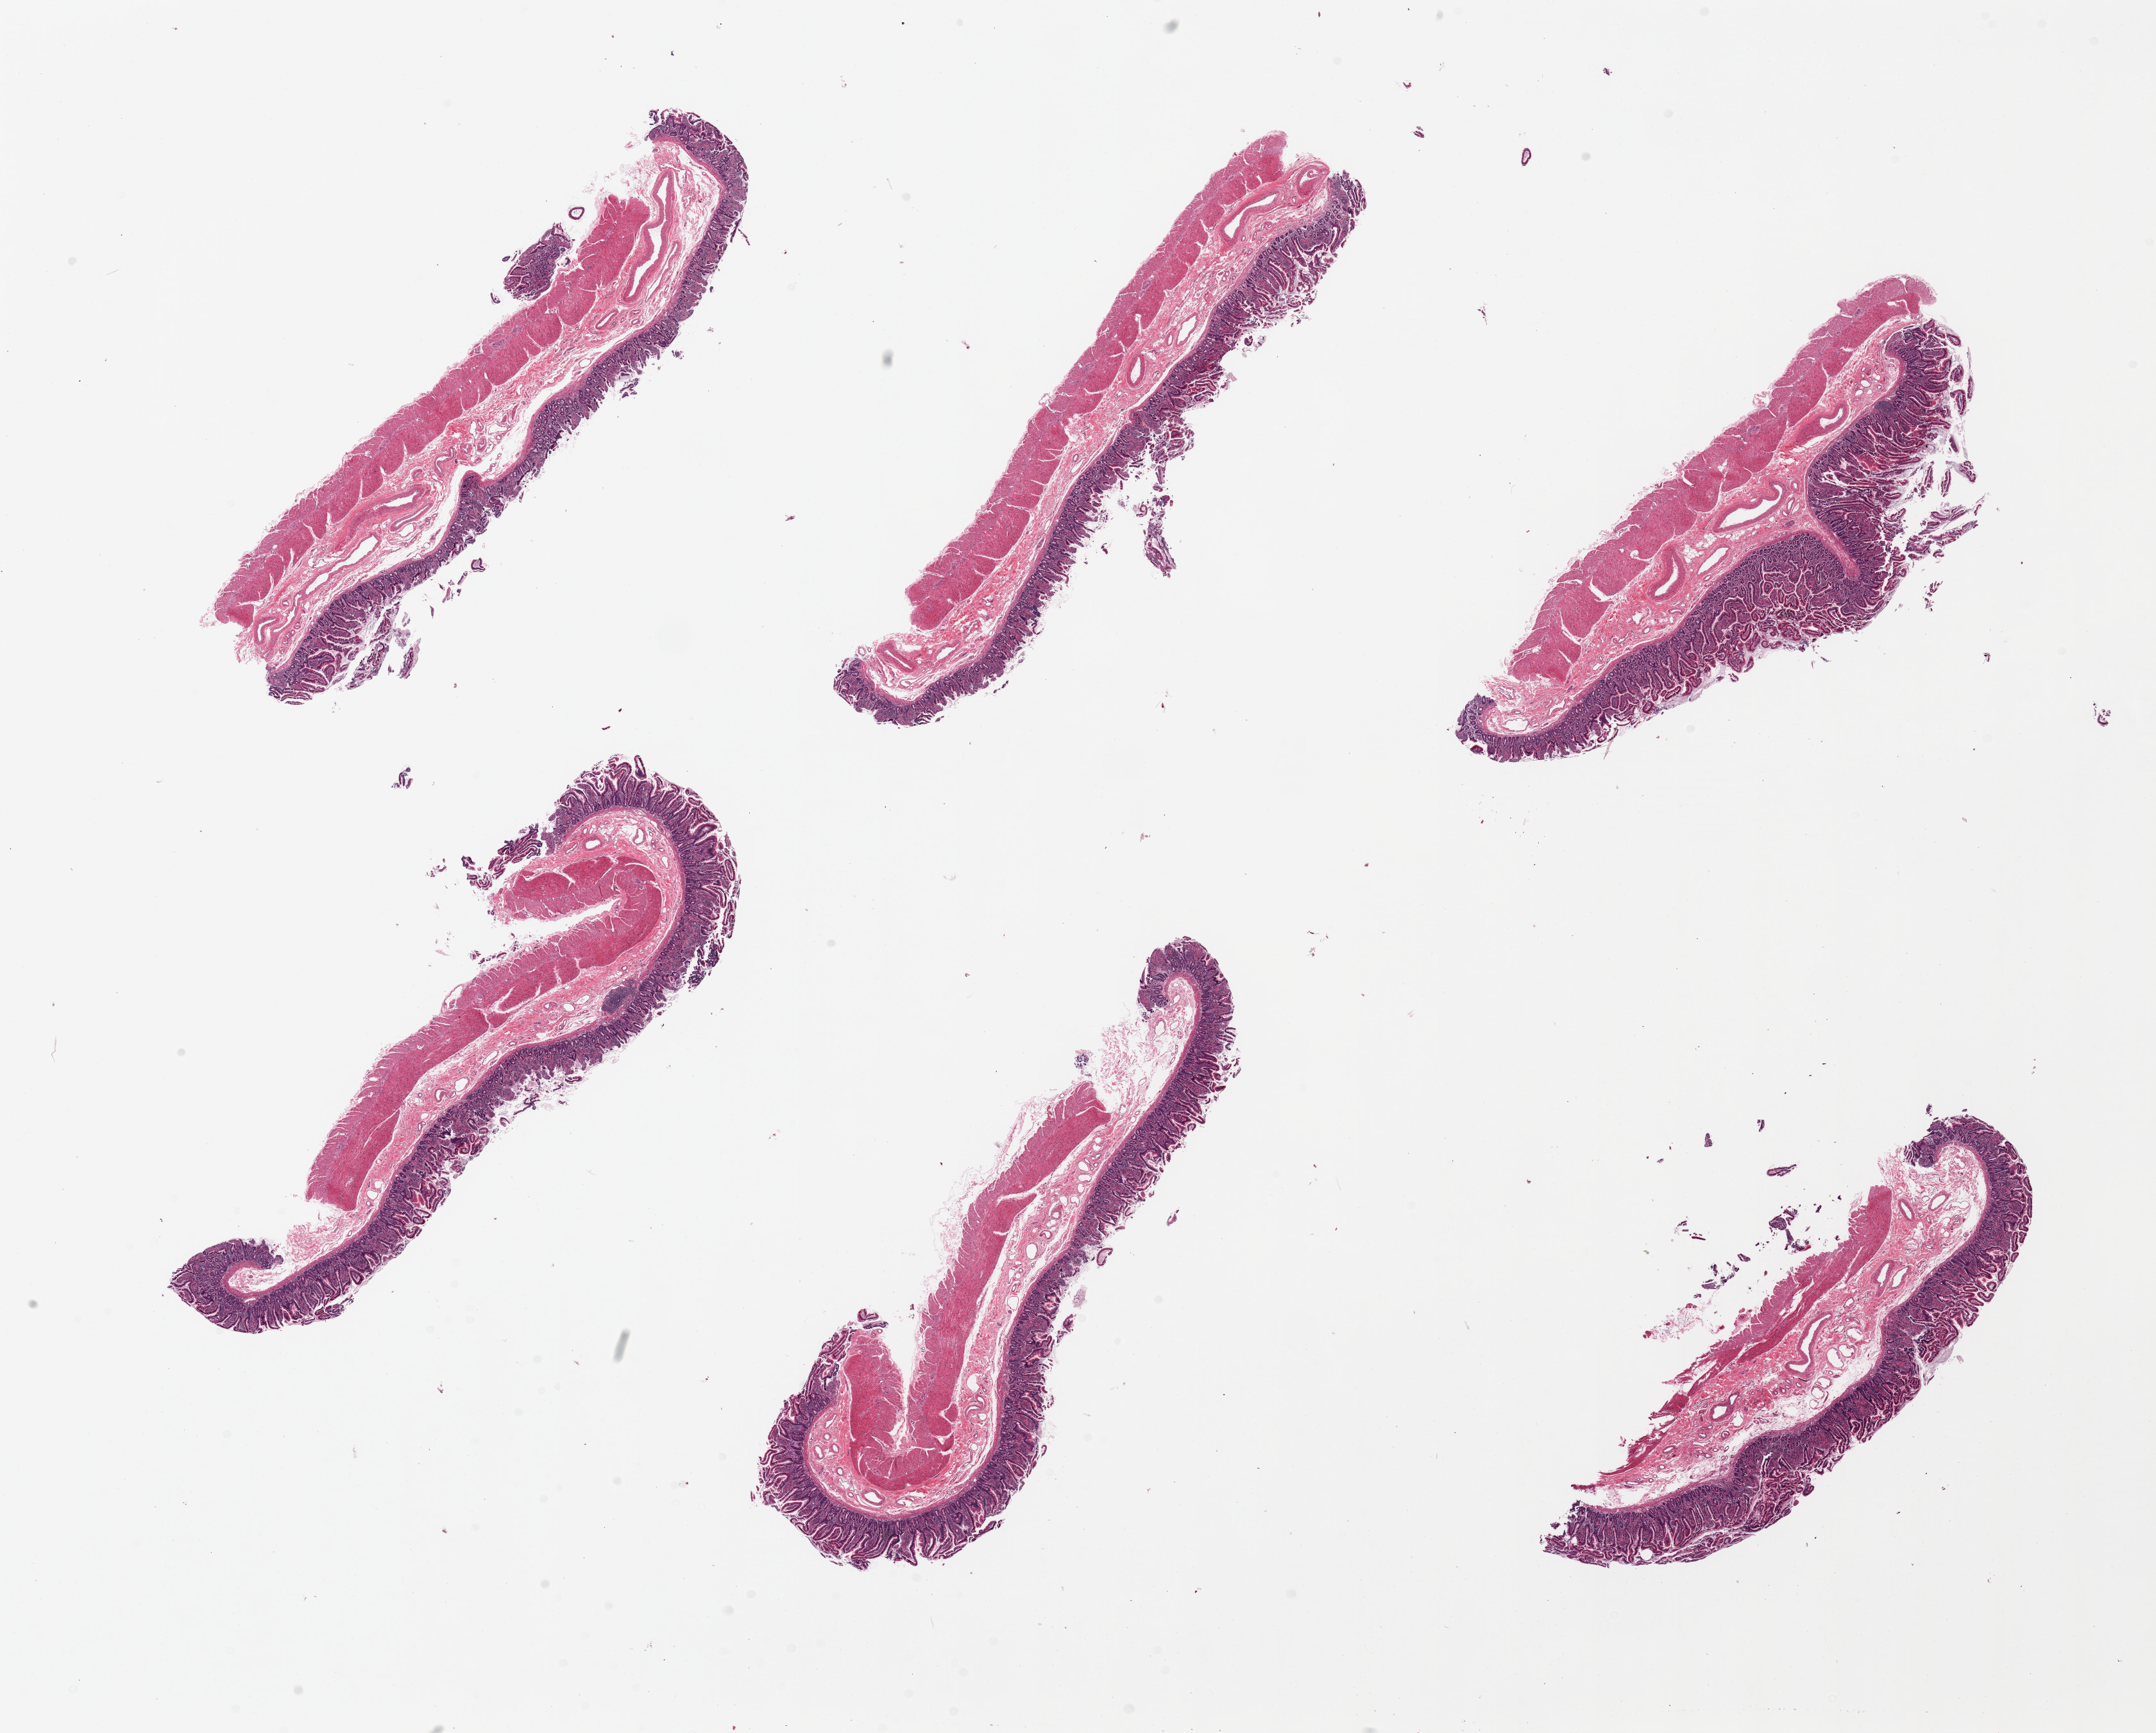
Digitized H&E-stained section — low-resolution overview of the scanned area, about 26.6 x 21.4 mm (acquisition: 20x scan); PAXgene-fixed, paraffin-embedded tissue; target tissue: transverse colon; donor tissue sample. Donor sex: male.
Review note (as recorded): 6 pieces. Small bowel not colon.